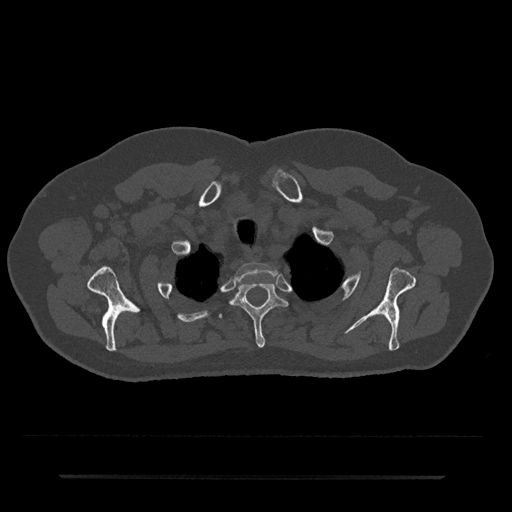
CT including the spine, one axial slice; reconstruction kernel Br40s/3; 120 kVp; bone window (W 1800 / L 400 HU); 0.5 mm slice thickness; 512 × 512 image matrix, field of view 437 × 437 mm. Male patient, age 69 years. From the clinical record (not read from this slice): primary cancer: prostate.
Outlined on this slice (semi-automatic segmentation, software-assisted and operator-edited):
- T1 vertebra: bounding box (x1, y1, x2, y2) in pixels: (235, 262, 279, 282)
- T2 vertebra: (230, 282, 288, 347)
- T3 vertebra: (219, 314, 222, 319)